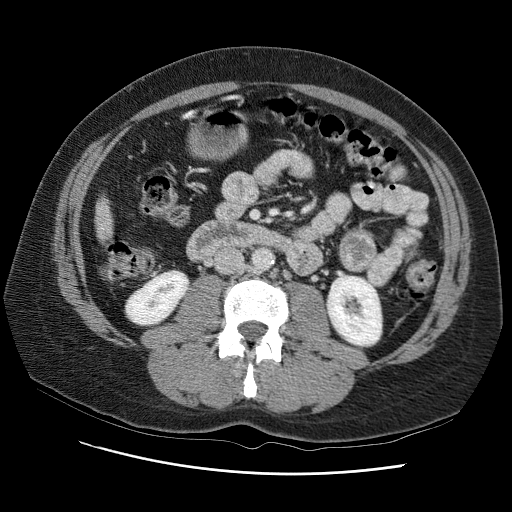
Contrast-enhanced abdominal CT (liver protocol), one axial slice; slice 19 of 95 in the series (ordered by position); reconstruction kernel STANDARD; 120 kVp; one of 2 acquisitions stored at this slice position; soft-tissue window (W 400 / L 40 HU); 2.5 mm slice thickness; 512 × 512 image matrix, field of view 360 × 360 mm. From the clinical record (not read from this slice): diagnosis: hepatocellular carcinoma (patient treated with transarterial chemoembolisation; whether this scan precedes or follows treatment is not stated here); TNM stage (as recorded): Stage-I; Child-Pugh class: B; tumour differentiation: moderately differentiated; tumour nodularity: uninodular.
Annotated regions visible in this slice (semi-automatic segmentation, software-assisted and operator-edited):
- liver parenchyma outside the tumour (the mass and vessels are separate outlines, so this box may not span the whole liver): bounding box [x1, y1, x2, y2] px = [96, 174, 128, 248]
- liver vessels: [116, 232, 119, 235]